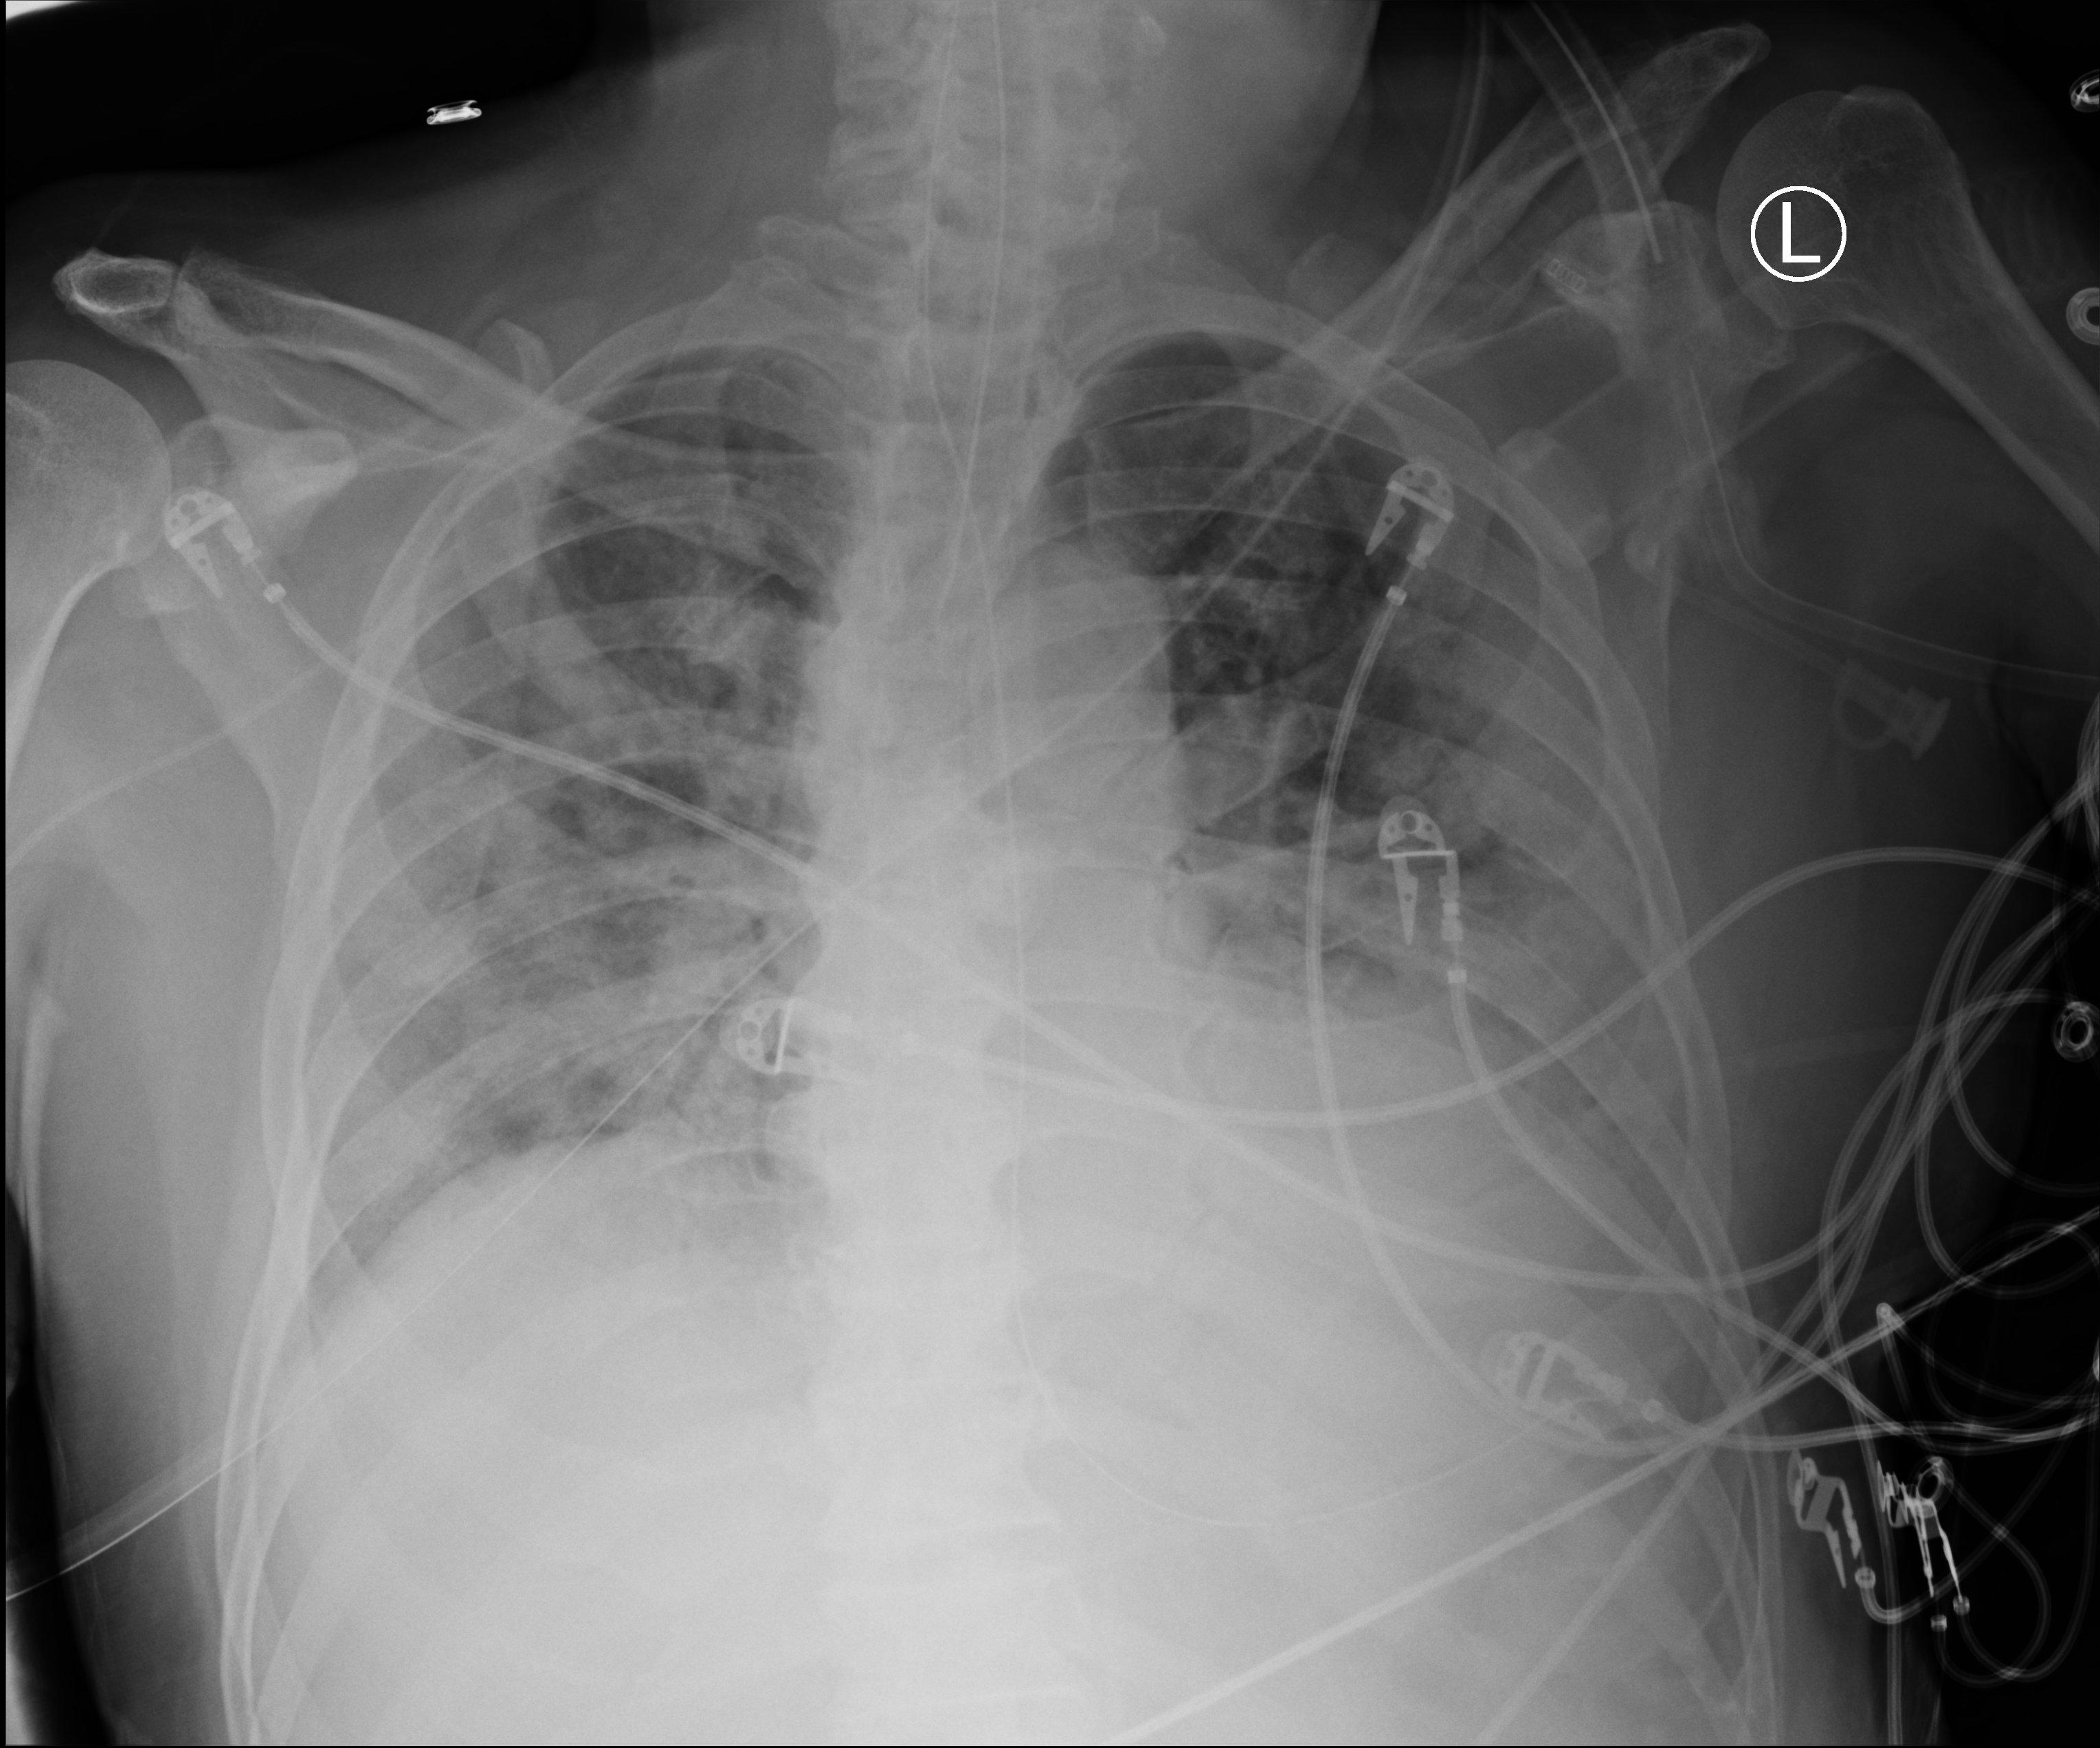
Portable chest radiograph, anteroposterior (AP) projection. Patient hospitalised with COVID-19; male, aged 75–90 years.
Admission-level facts for this patient (not findings on this image; timing relative to this image not recorded): admitted to intensive care during this hospital stay: yes; other chronic lung disease (admission record): no.